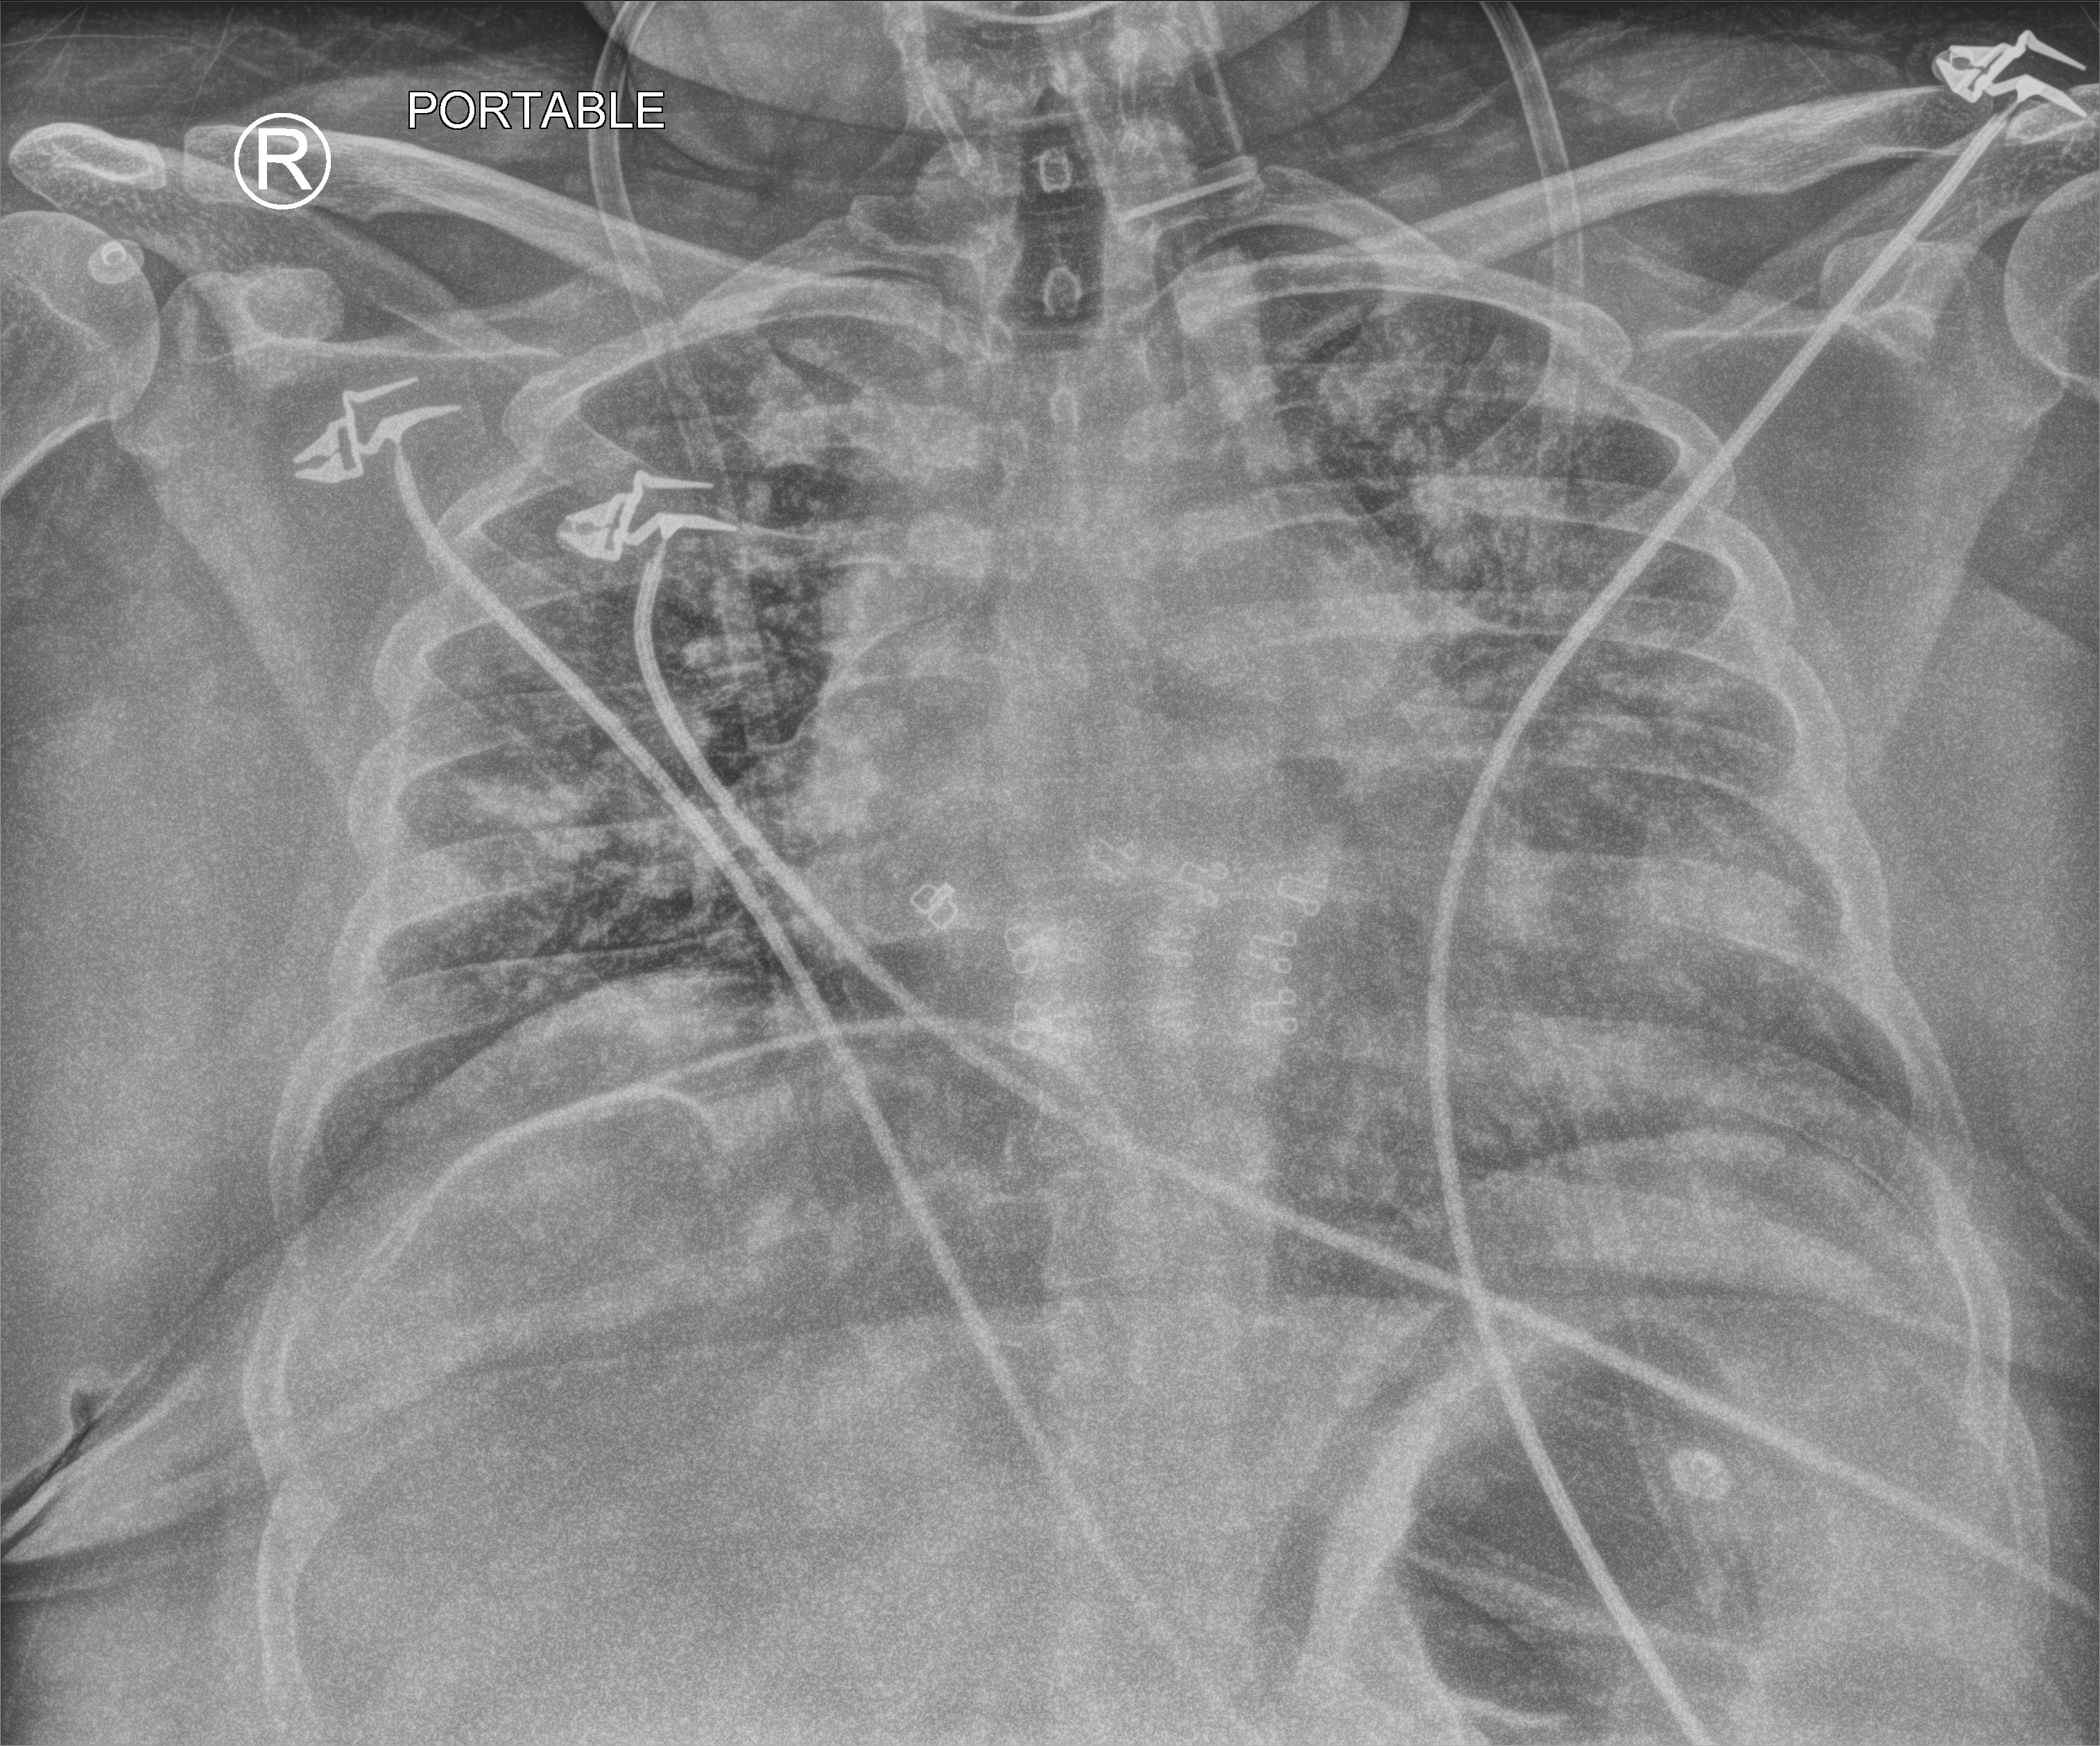
Chest X-ray (portable), anteroposterior (AP) projection. Patient hospitalised with COVID-19; female, aged 18–59 years.
From the hospital-stay record, not from the radiograph (when in the stay this image was taken is not recorded):
- mechanically ventilated during this hospital stay: no